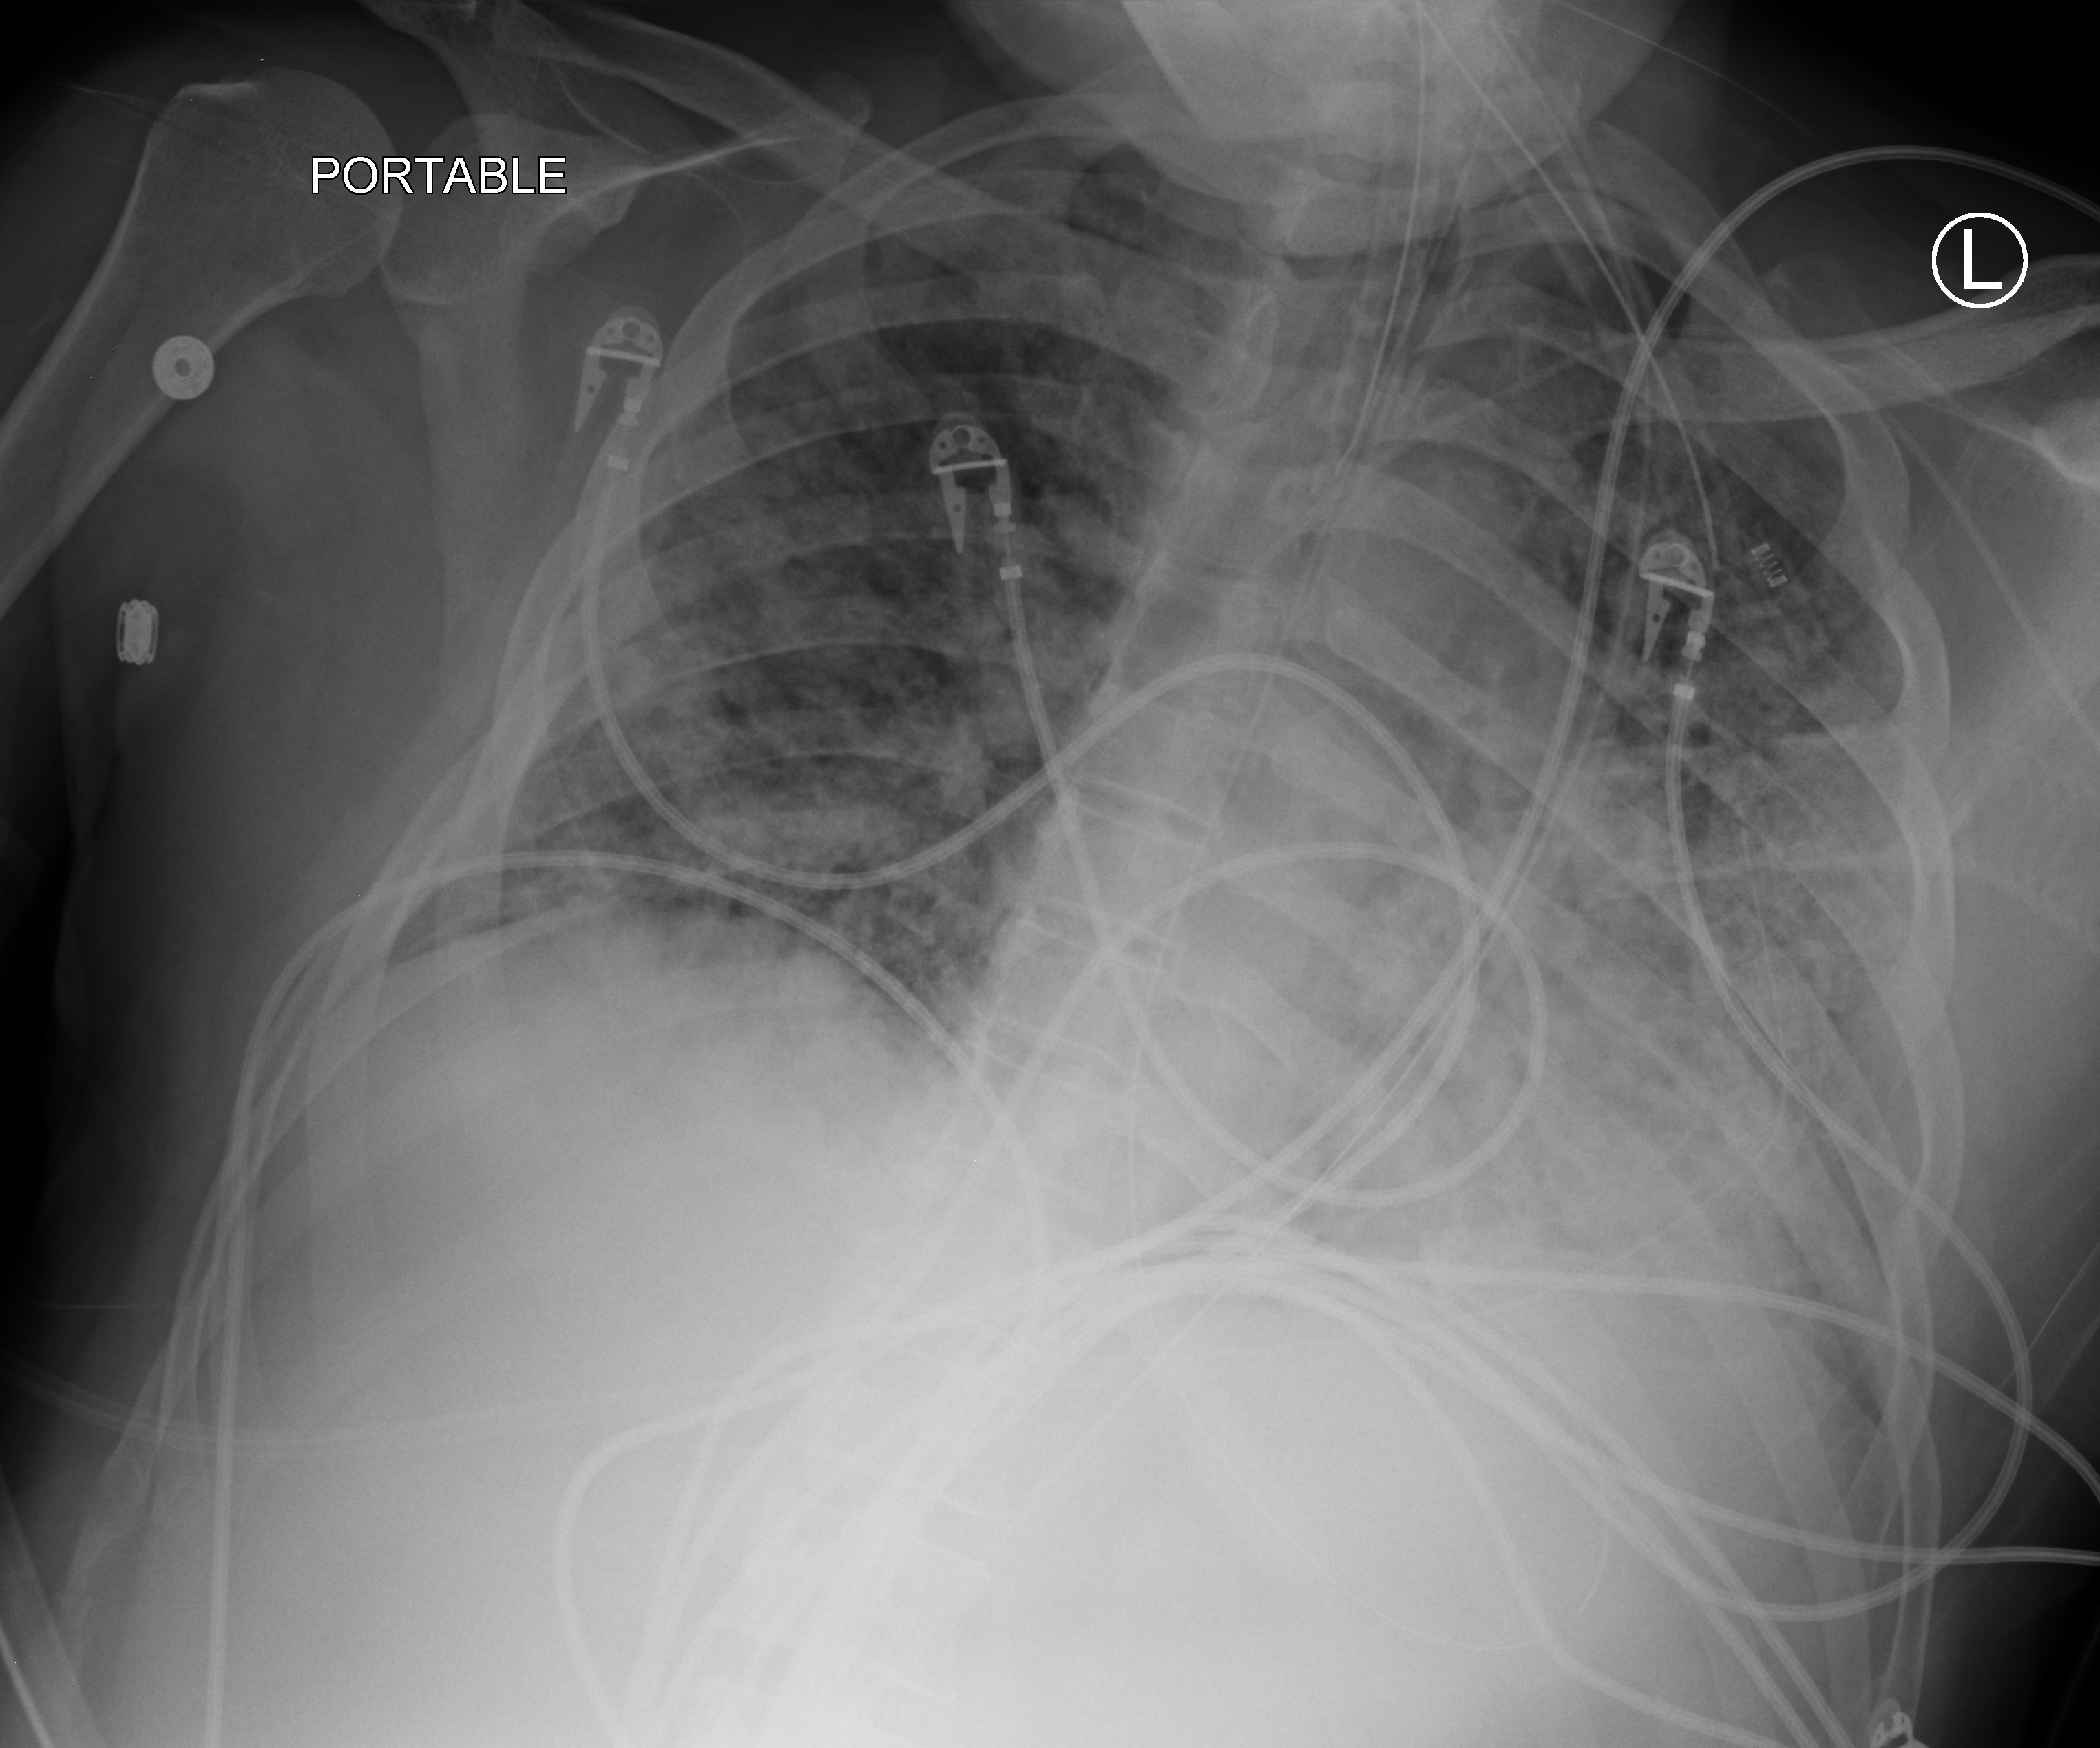
Chest X-ray (portable); anteroposterior (AP) projection. Male patient hospitalised with COVID-19, age 18–59 years.
Admission-level facts for this patient (not findings on this image; timing relative to this image not recorded): other chronic lung disease (admission record): no; admitted to intensive care during this hospital stay: yes; mechanically ventilated during this hospital stay: yes.